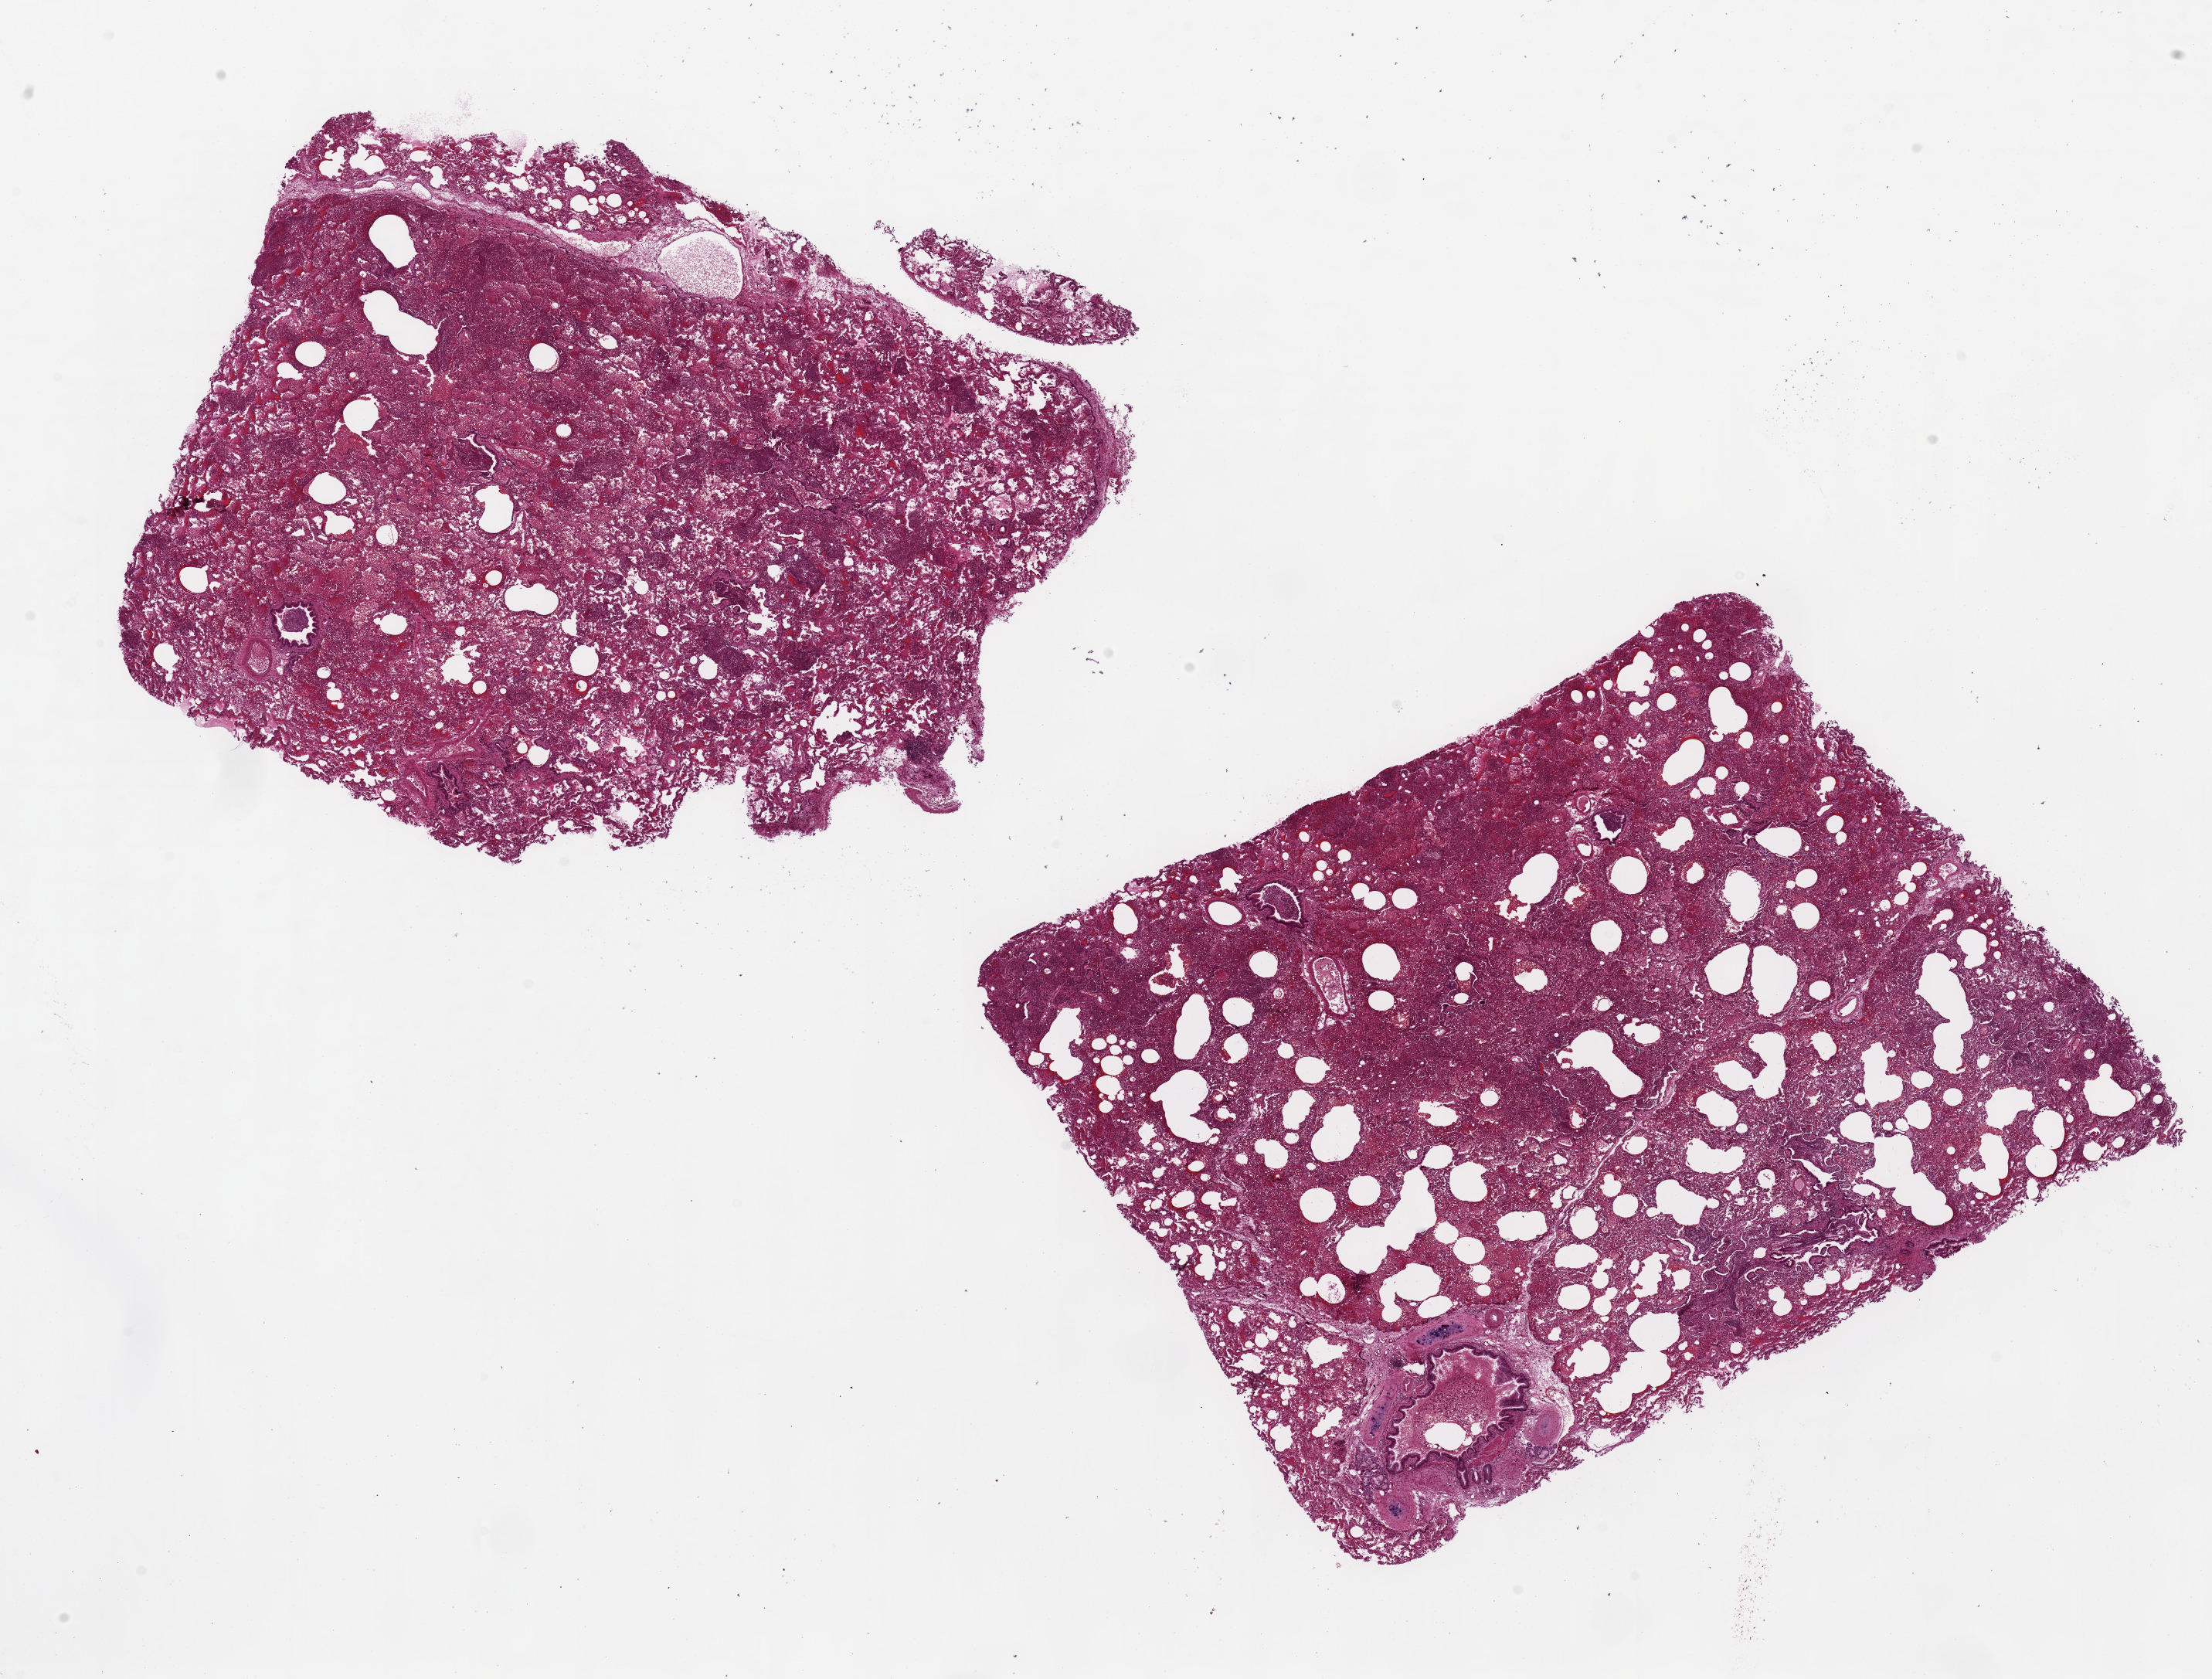
Hematoxylin and eosin (H&E) whole-slide image, brightfield, low-resolution overview of the scanned area, about 22.6 x 17.2 mm (from a 20x scan); PAXgene-fixed paraffin-embedded (PFPE) section; target tissue: lung; donor tissue sample. Donor: male.
Review note (as recorded): 2 pieces ~9x7 mm; extensive bronchopneumonia.